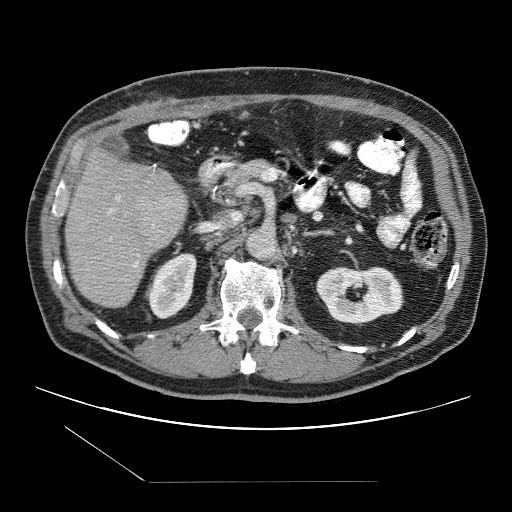
Contrast-enhanced abdominal CT (liver protocol), one axial slice. Slice 41 of 109 in the series (ordered by position). 120 kVp. One of 2 acquisitions stored at this slice position. Soft-tissue window (W 400 / L 40 HU). 2.5 mm slice thickness. 512 × 512 image matrix, field of view 400 × 400 mm. From the clinical record (not read from this slice): diagnosis: hepatocellular carcinoma (patient treated with transarterial chemoembolisation; whether this scan precedes or follows treatment is not stated here); TNM stage (as recorded): Stage-IIIB; Child-Pugh class: A; tumour nodularity: multinodular.
Structures marked on this image (semi-automatically segmented with operator editing):
- liver parenchyma outside the tumour (the mass and vessels are separate outlines, so this box may not span the whole liver): bounding box <64,148,188,308> (left, top, right, bottom; pixels)
- liver vessels: <108,166,159,268>